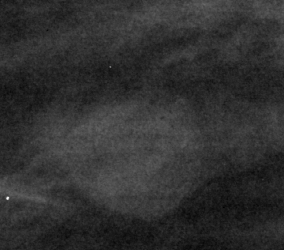
Crop from a digitized film mammogram around one marked abnormality, right breast, MLO view.
Finding: mass, shape round, margins circumscribed; BI-RADS assessment category 3; pathology (as recorded): benign.